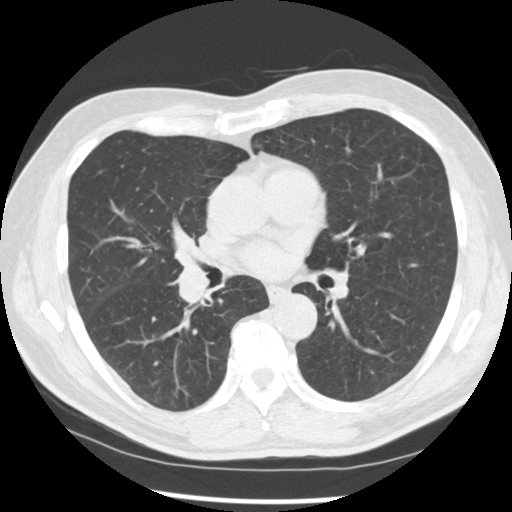
Low-dose screening chest CT, axial slice, baseline annual screen, lung window (W 1500 / L -600 HU), standard (soft-tissue) reconstruction kernel (STANDARD), 512 × 512 image matrix. Male, age 67 years at enrolment. Current smoker at enrolment.
Expert-annotated lung lesion, box from (x=159, y=247) to (x=229, y=312) px. The exam's reader record, not a measurement of the box and not confirmed to be the same lesion: non-calcified nodule or mass ≥4 mm, left lower lobe, 15 × 15 mm, spiculated (stellate) margins, soft tissue attenuation. Note: the box lies in the patient's right hemithorax on this image, whereas the reader's record names the left lung; they may be different findings. Official screen result: positive, change unspecified: nodule(s) >= 4 mm or enlarging nodule(s), mass(es), or other non-specific abnormalities suspicious for lung cancer.